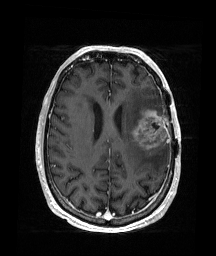
Brain MRI from a brain-tumour surgery series, one axial slice; position 70 of 176 along the scan axis; T1-weighted post-contrast; 1 mm slice thickness; 216 × 256 image matrix, field of view 219 × 260 mm. Case-level facts recorded for this patient, not image findings: histopathology: Glioblastoma; WHO grade: 4; IDH mutation: no.
Annotated regions visible in this slice (manually delineated by an expert):
- tumour: bounding box [x1, y1, x2, y2] px = [132, 109, 168, 150]